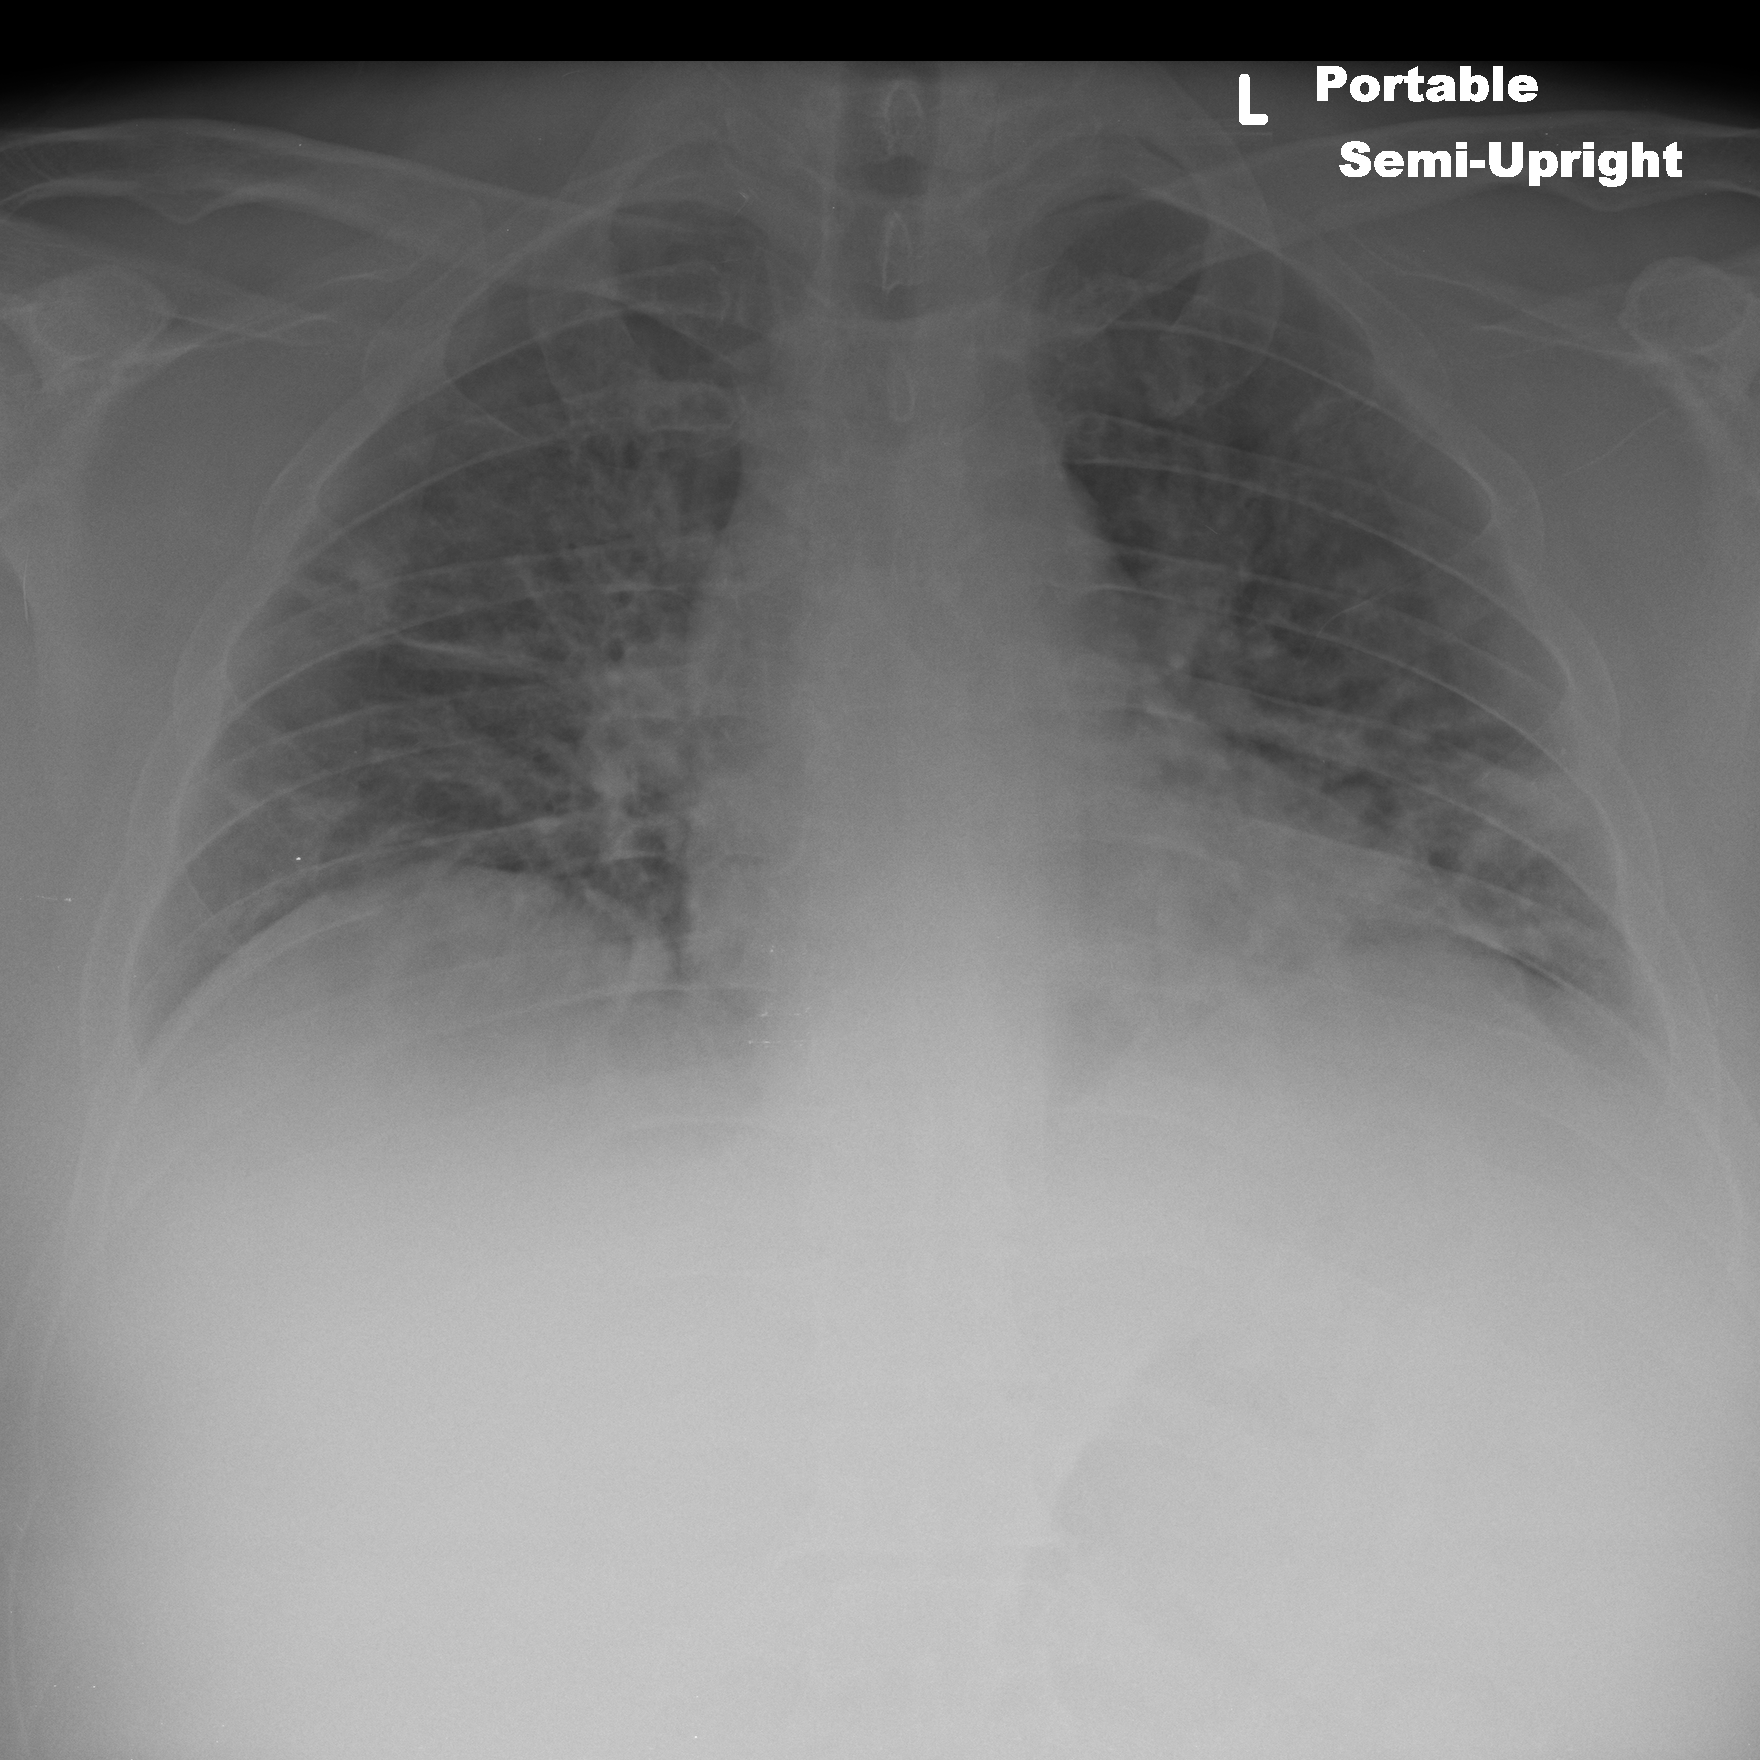
Chest X-ray, AP projection. Male patient, age 40 years; COVID-19 (test-positive).
Radiologist's key findings for this exam: Patchy opacities are noted at lung bases greater on left than right. There appears to be very slight worsening on left, no change on right. No large effusion noted.